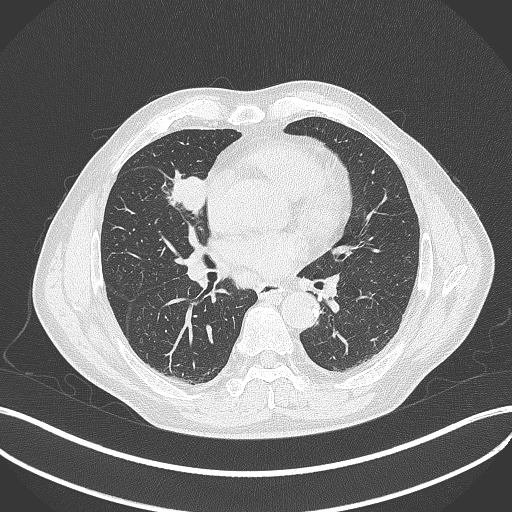
Chest CT, one axial slice. Slice 197 of 429 in the series (ordered by position). Reconstruction kernel B70f. 120 kVp. Lung window (W 1500 / L -600 HU). 1 mm slice thickness. 512 × 512 image matrix, field of view 400 × 400 mm. Male patient, age 61 years. From the clinical record (not read from this slice): clinical TNM (as recorded): T2b N1 M0.
Structures marked on this image (bounding box drawn by a radiologist):
- lung tumour (recorded histology: squamous cell carcinoma): bounding box [x1, y1, x2, y2] px = [165, 167, 207, 221]